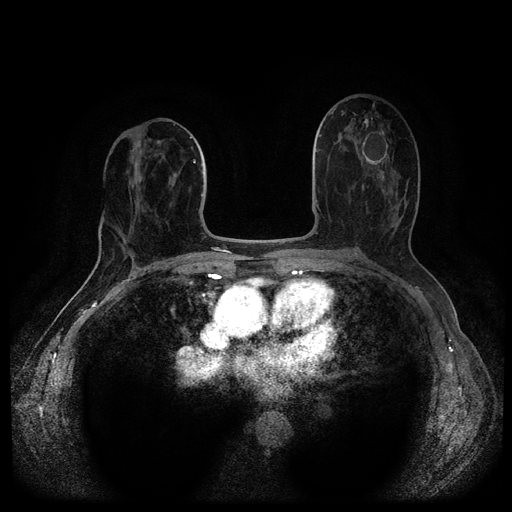
Breast MRI (dynamic contrast-enhanced, multi-phase), one axial slice. Position 53 of 116 along the scan axis. Dynamic contrast-enhanced series, time point 2 of 5 at this slice position (early post-contrast). 1.5 T. TE 2.6 ms, TR 5.4 ms. 512 × 512 image matrix, field of view 340 × 340 mm. Patient: female, 69 years.
Structures marked on this image (semi-automatically segmented with operator editing):
- breast lesion (labelled benign in the annotation): bounding box [x1, y1, x2, y2] px = [359, 131, 389, 167]